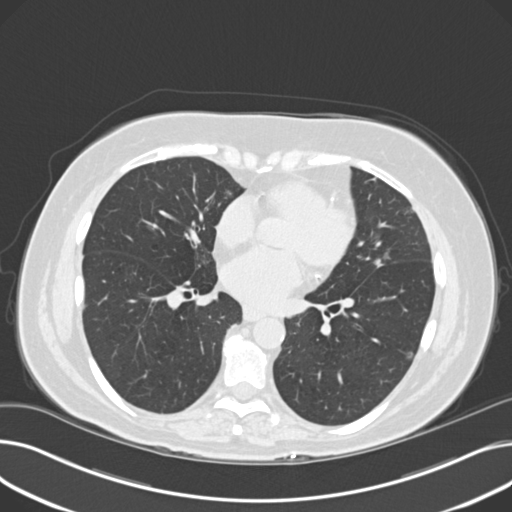
Low-dose screening chest CT, one axial slice; position 88 of 203 along the scan axis; 120 kVp; lung window (W 1500 / L -600 HU); 2 mm slice thickness; 512 × 512 image matrix.
Structures marked on this image (outlined manually by an expert reader):
- lesion 1 (tumor, upper lobe of left lung): box from (x=374, y=258) to (x=383, y=267) px